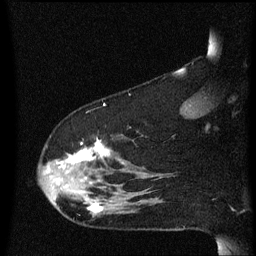
Breast MRI (dynamic contrast-enhanced), one sagittal slice. Slice 47 of 60 in the series (ordered by position). Dynamic contrast-enhanced series, image 2 of 3 at this slice position (ordered by acquisition). 1.5 T. TE 4.2 ms, TR 8.4 ms. 2 mm slice thickness. 256 × 256 image matrix, field of view 200 × 200 mm. Patient: female, 48 years.
Structures marked on this image (semi-automatic segmentation, software-assisted and operator-edited):
- analysis volume of interest (the breast-tissue region the enhancement analysis was run in; not a lesion): box from (x=39, y=140) to (x=134, y=219) px
- tumour enhancement mask (voxels above the 70 % enhancement threshold inside the analysis volume of interest): (x=57, y=142)–(x=108, y=213)